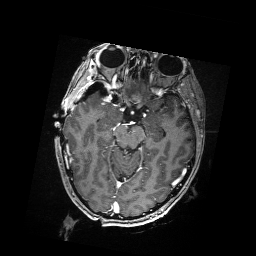
Brain MRI from a brain-tumour surgery series, one axial slice; slice 110 of 176 in the series (ordered by position); T1-weighted post-contrast; 1 mm slice thickness; 256 × 256 image matrix. Case-level facts recorded for this patient, not image findings: histopathology: Metastatic Carcinoma from Breast primary; tumour location: Right Frontal.
Structures marked on this image (expert manual segmentation):
- residual tumour: bounding box (x1, y1, x2, y2) in pixels: (88, 88, 117, 96)